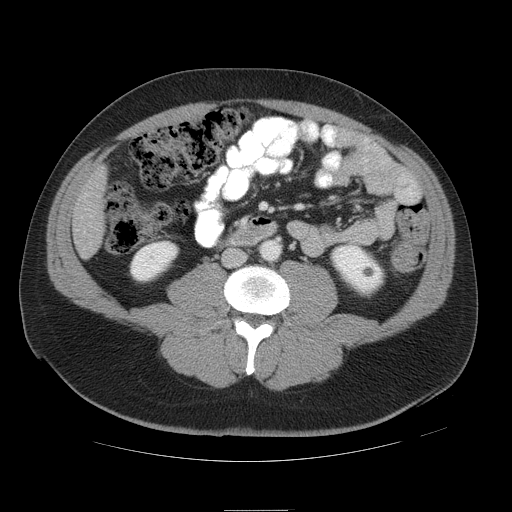
Contrast-enhanced abdominal CT, one axial slice. Slice 11 of 49 in the series (ordered by position). Reconstruction kernel STANDARD. 120 kVp. Intravenous contrast given. Soft-tissue window (W 400 / L 40 HU). 5 mm slice thickness. 512 × 512 image matrix, field of view 425 × 425 mm. Male patient, age 52 years. From the clinical record (not read from this slice): diagnosis: colorectal cancer liver metastases, imaged before liver resection; multiple liver metastases: yes; largest metastasis: 5.1 cm.
Outlined on this slice (manually delineated by an expert):
- liver: bounding box <74,172,107,257> (left, top, right, bottom; pixels)